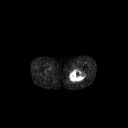
FDG PET of an extremity soft-tissue mass (from a PET/CT study), one axial slice; position 254 of 267 along the scan axis; 3.27 mm slice thickness; 128 × 128 image matrix, field of view 700 × 700 mm. Patient: male, 44 years. Case-level facts recorded for this patient, not image findings: histological type: undifferentiated pleomorphic liposarcoma; grade: high; site of the primary tumour: left thigh.
Structures marked on this image (expert contour drawn on MRI and transferred to this co-registered scan by the dataset authors):
- gross tumour volume including surrounding oedema: bounding box [x1, y1, x2, y2] px = [68, 70, 84, 83]
- gross tumour volume (mass): [70, 70, 84, 81]